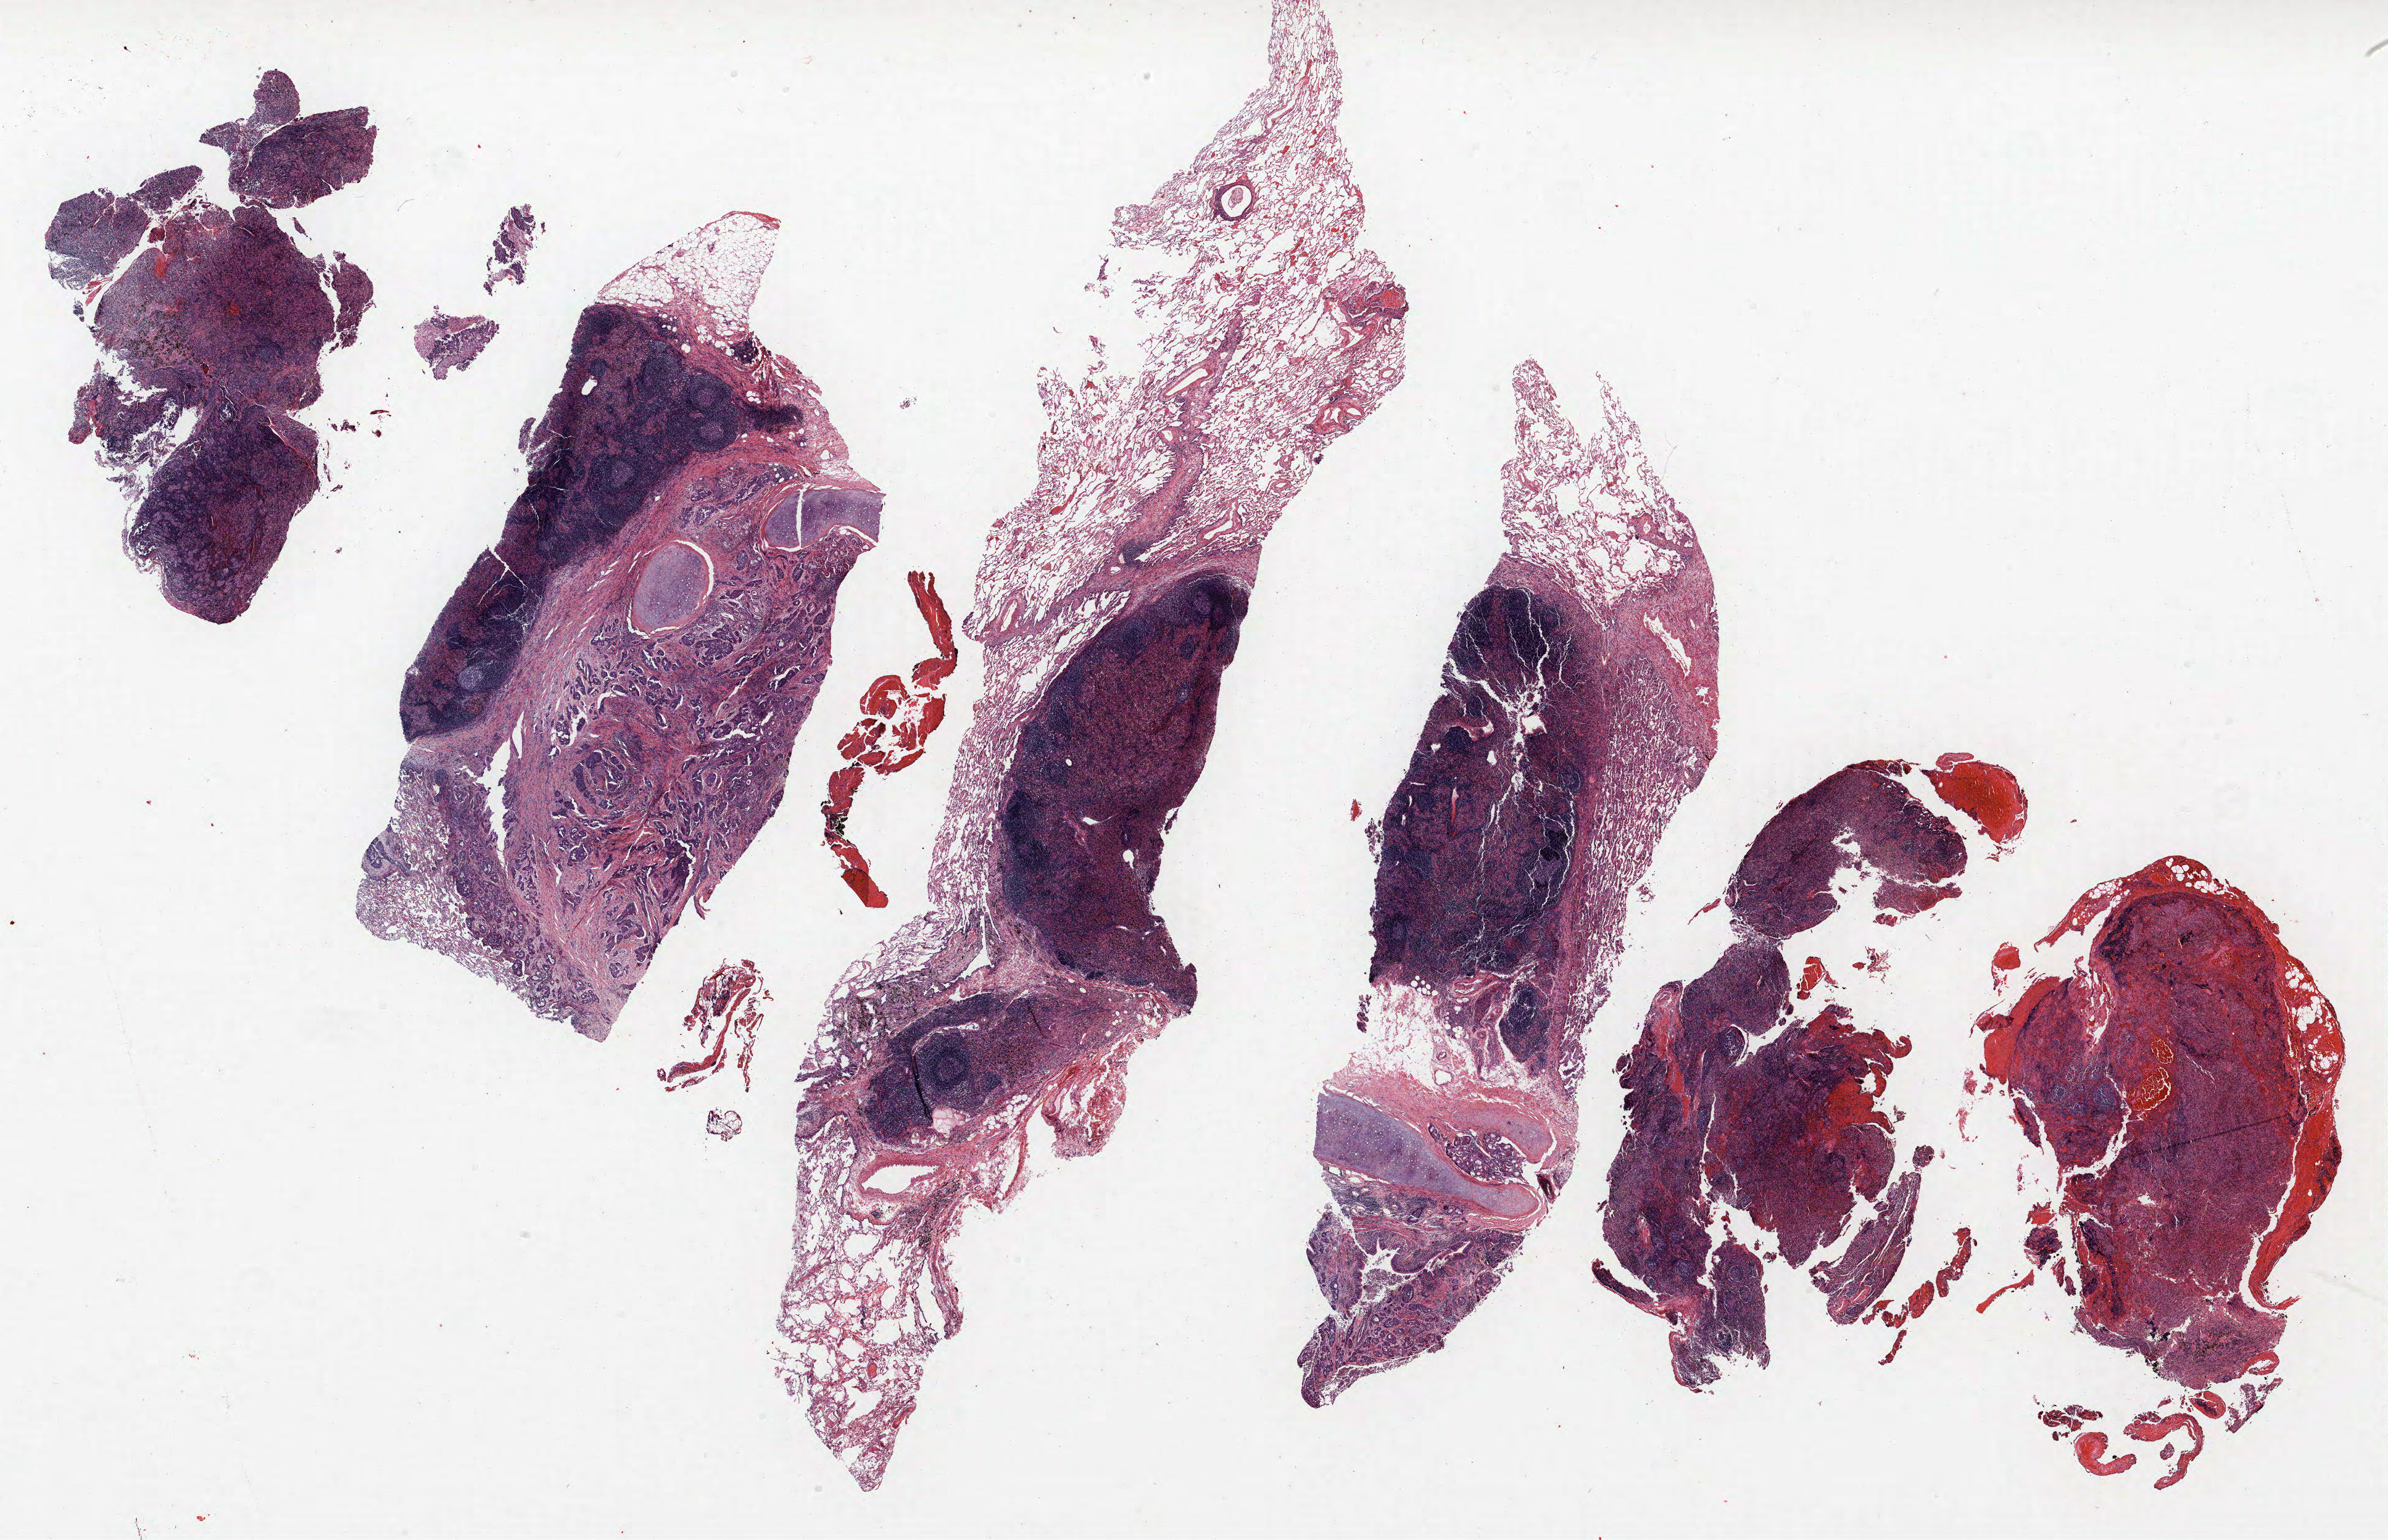
Whole-slide histology image, H&E, whole scanned area (about 31.0 x 20.0 mm) shown as a low-resolution overview; FFPE section; lung tissue. Male, age 57 at enrolment. Former smoker at enrolment. Grade: poorly differentiated (G3).
* primary tumour location (clinical record): right upper lobe
* stage (AJCC 6th edition): IIA
* participant's lung-cancer diagnosis: Squamous cell carcinoma, NOS
* tumour size (pathology): 30 mm